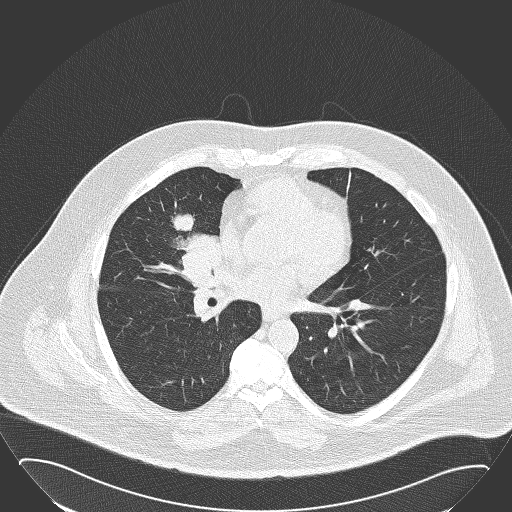
Low-dose screening chest CT, axial slice, first (baseline) screen, lung window (W 1500 / L -600 HU), lung (sharp) reconstruction kernel (B50f). Male, age 61 years at enrolment. Former smoker at enrolment.
Expert reader's lesion annotation, box from (x=146, y=203) to (x=231, y=289) px. The screening reader recorded 2 non-calcified nodules or masses ≥4 mm on this exam; which of them this box marks is not recorded.